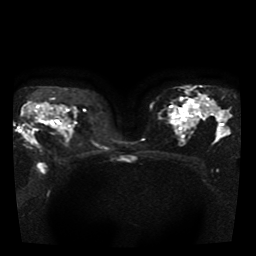
Breast MRI, one axial slice; position 25 of 41 along the scan axis; diffusion-weighted series; image 2 of 4 stored at this slice position (different b-values; order by instance number); 1.5 T; 5 mm slice thickness; 256 × 256 image matrix, field of view 330 × 330 mm. Female patient.
Structures marked on this image (manually delineated by an expert):
- tumour on diffusion-weighted imaging: bounding box <23,104,51,145> (left, top, right, bottom; pixels)